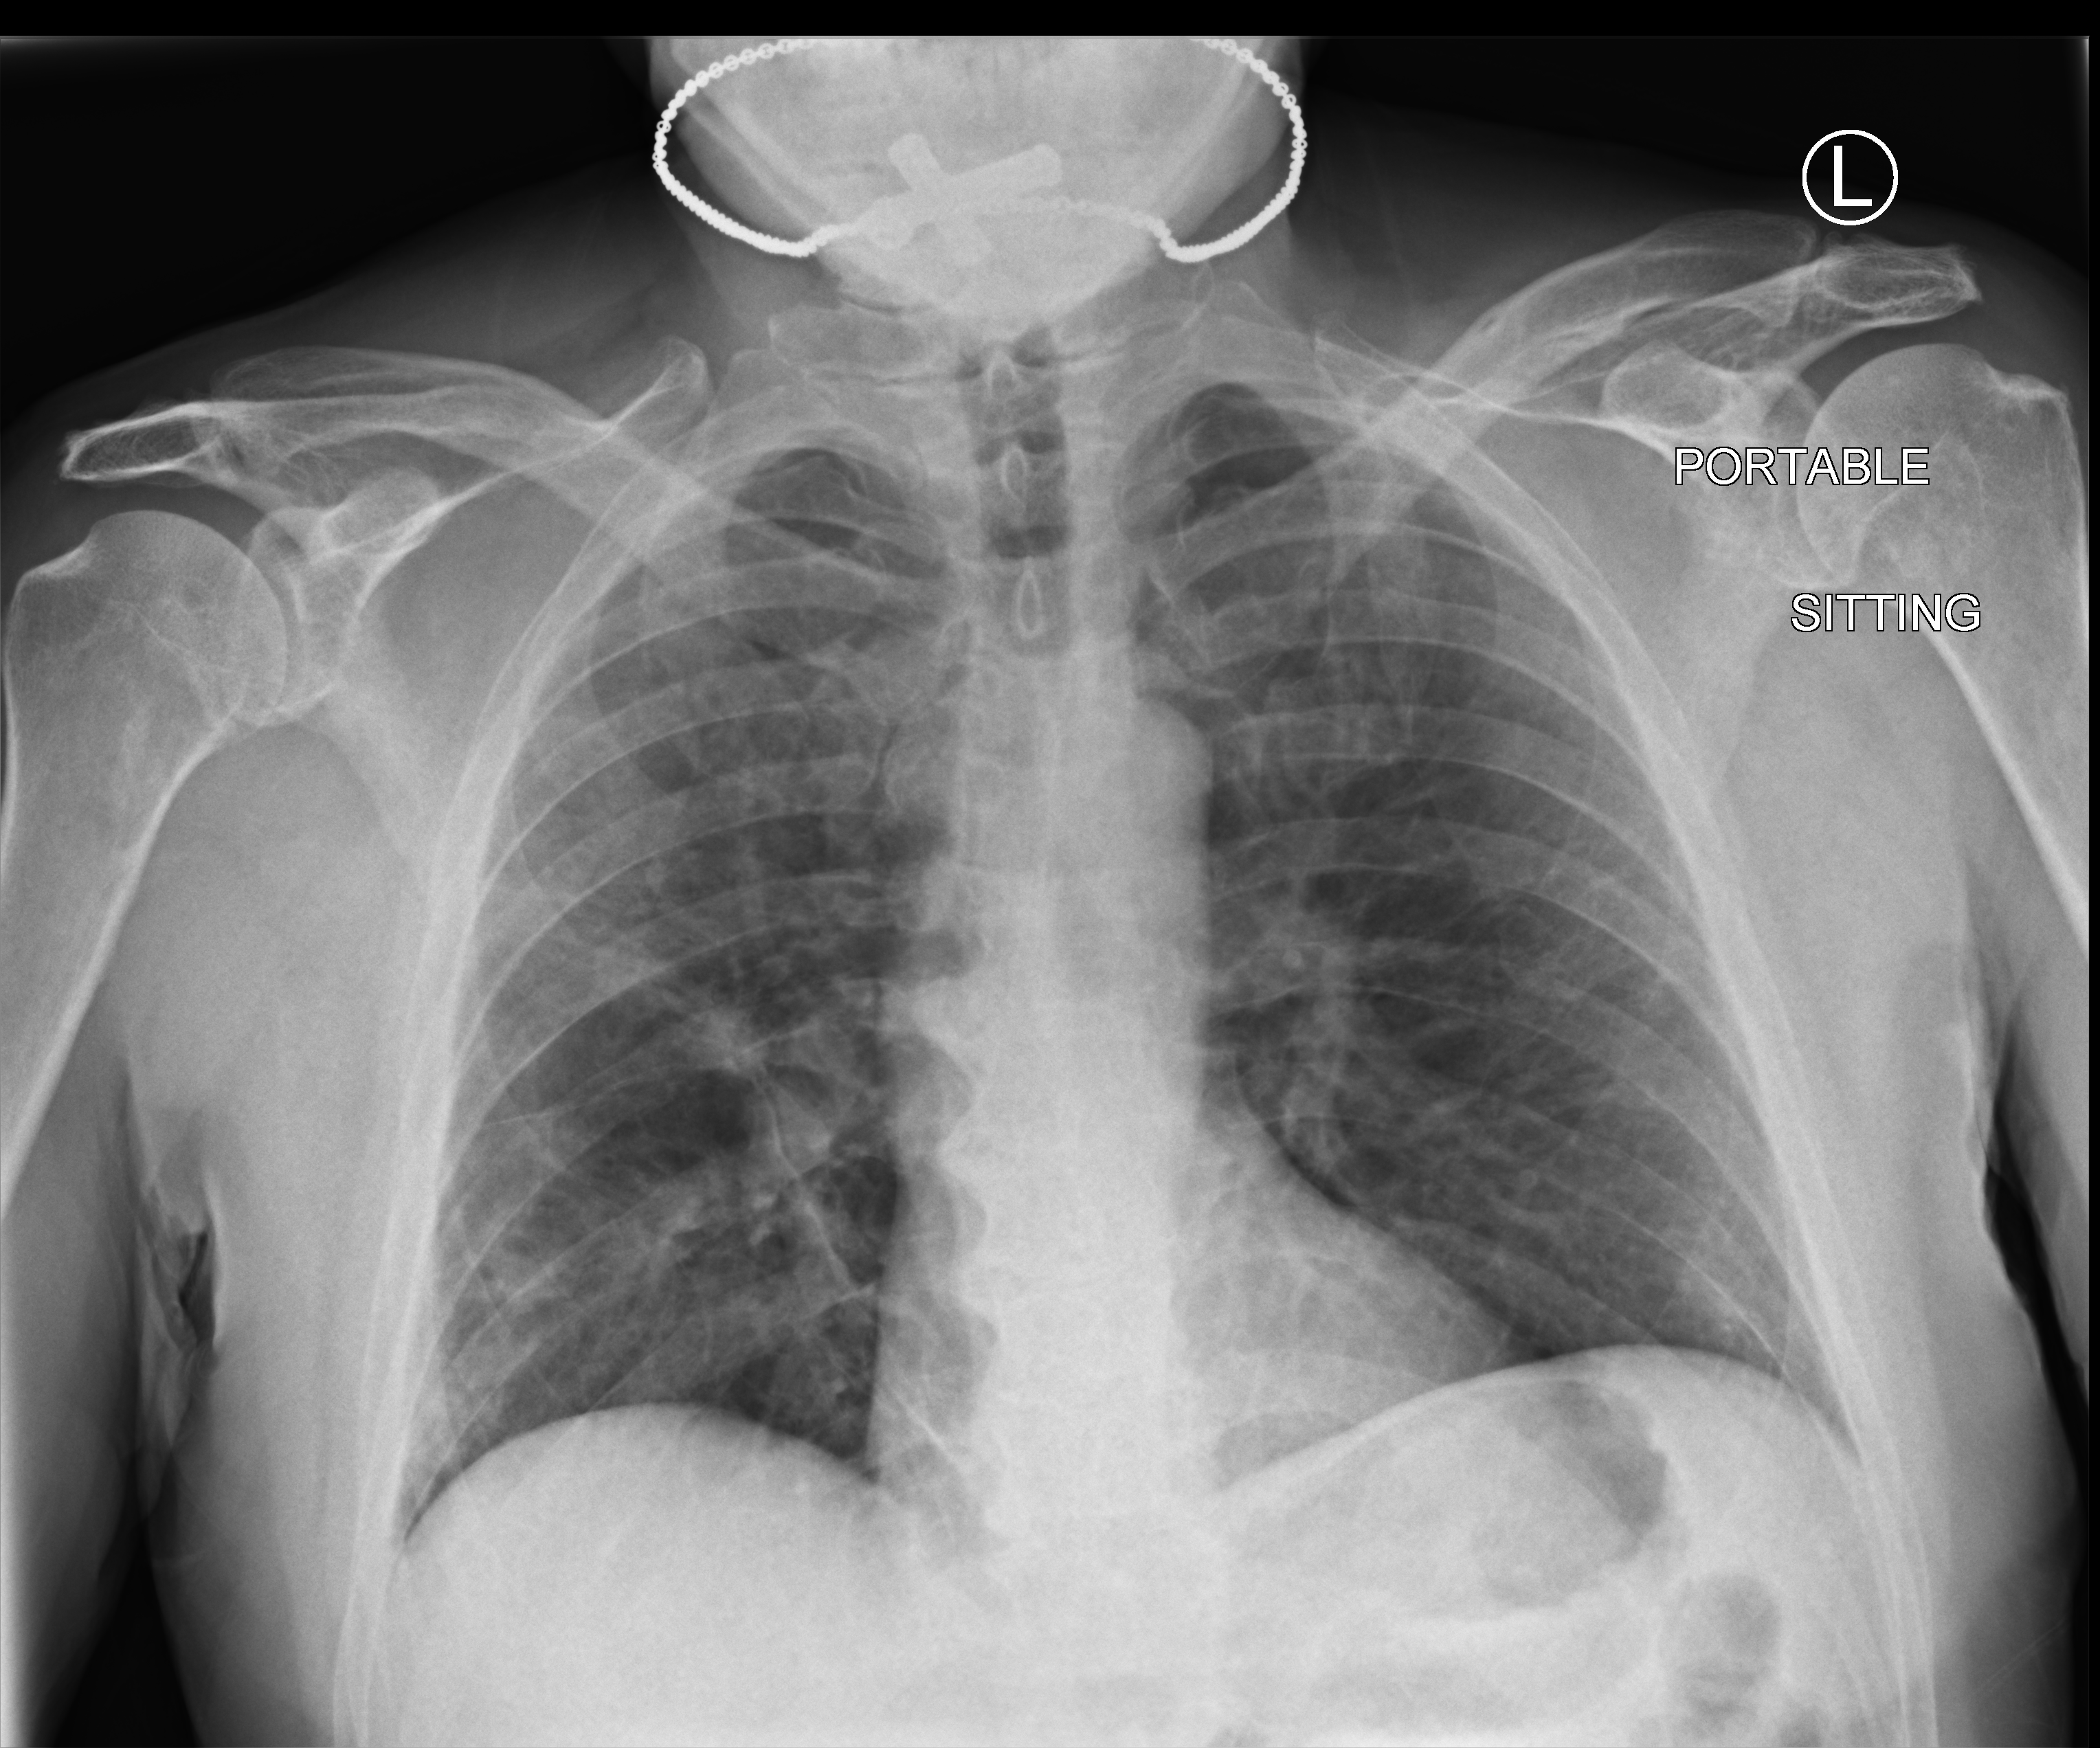
Portable chest radiograph, anteroposterior (AP) projection. Patient hospitalised with COVID-19; male, aged 18–59 years.
From the hospital-stay record, not from the radiograph (when in the stay this image was taken is not recorded):
- length of hospital stay: 5 days
- chronic kidney disease (admission record): no
- mechanically ventilated during this hospital stay: no